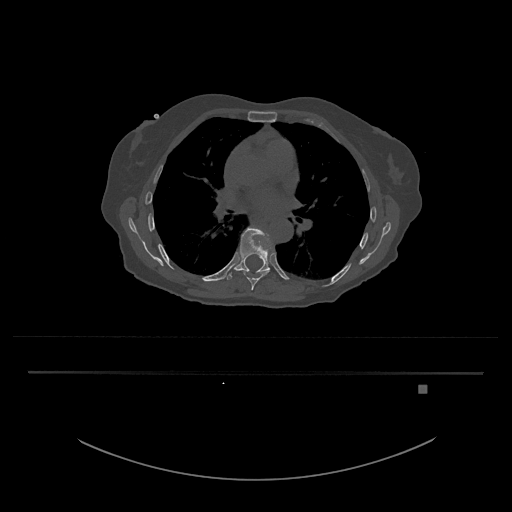
CT including the spine, one axial slice; slice 780 of 797 in the series (ordered by position); reconstruction kernel Br40s/3; 120 kVp; bone window (W 1800 / L 400 HU); 512 × 512 image matrix, field of view 500 × 500 mm. Female patient, age 57 years. Case-level facts recorded for this patient, not image findings: primary cancer: cervical.
Outlined on this slice (semi-automatic segmentation, software-assisted and operator-edited):
- T8 vertebra: bounding box (x1, y1, x2, y2) in pixels: (243, 270, 268, 290)
- T9 vertebra: (224, 227, 274, 280)